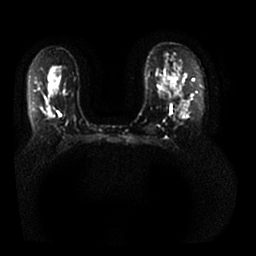
Breast MRI, one axial slice. Slice 20 of 25 in the series (ordered by position). Diffusion-weighted series; image 2 of 4 stored at this slice position (different b-values; order by instance number). 1.5 T. 4 mm slice thickness. 256 × 256 image matrix, field of view 350 × 350 mm. Female patient.
Structures marked on this image (manually delineated by an expert):
- tumour on diffusion-weighted imaging: bounding box <47,112,52,119> (left, top, right, bottom; pixels)